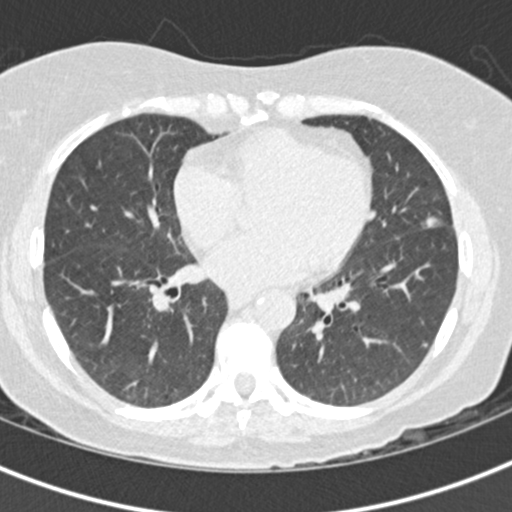
Low-dose screening chest CT, one axial slice. Reconstruction kernel B30f. Lung window (W 1500 / L -600 HU). 2 mm slice thickness. 512 × 512 image matrix.
Structures marked on this image (outlined manually by an expert reader):
- lesion 1 (tumor, lingular bronchus): bounding box <427,218,437,227> (left, top, right, bottom; pixels)